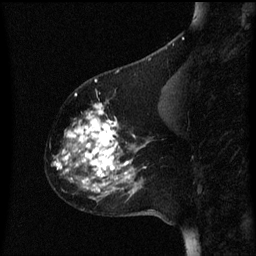
Breast MRI (dynamic contrast-enhanced), one sagittal slice. Slice 22 of 60 in the series (ordered by position). Dynamic contrast-enhanced series, image 2 of 3 at this slice position (ordered by acquisition). 1.5 T. TE 4.2 ms, TR 8 ms. 256 × 256 image matrix. Patient: female, 60 years.
Annotated regions visible in this slice (semi-automatic segmentation, software-assisted and operator-edited):
- analysis volume of interest (the breast-tissue region the enhancement analysis was run in; not a lesion): bounding box <52,100,151,197> (left, top, right, bottom; pixels)
- tumour enhancement mask (voxels above the 70 % enhancement threshold inside the analysis volume of interest): <54,106,147,193>